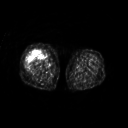
FDG PET of an extremity soft-tissue mass (from a PET/CT study), one axial slice; slice 227 of 311 in the series (ordered by position); 128 × 128 image matrix, field of view 500 × 500 mm. Female patient, age 57 years. Case-level facts recorded for this patient, not image findings: histological type: pleiomorphic undifferentiated sarcoma; grade: high; site of the primary tumour: right quadricep.
Outlined on this slice (expert contour drawn on MRI and transferred to this co-registered scan by the dataset authors):
- tumour plus oedema (research contour): box from (x=26, y=50) to (x=44, y=69) px